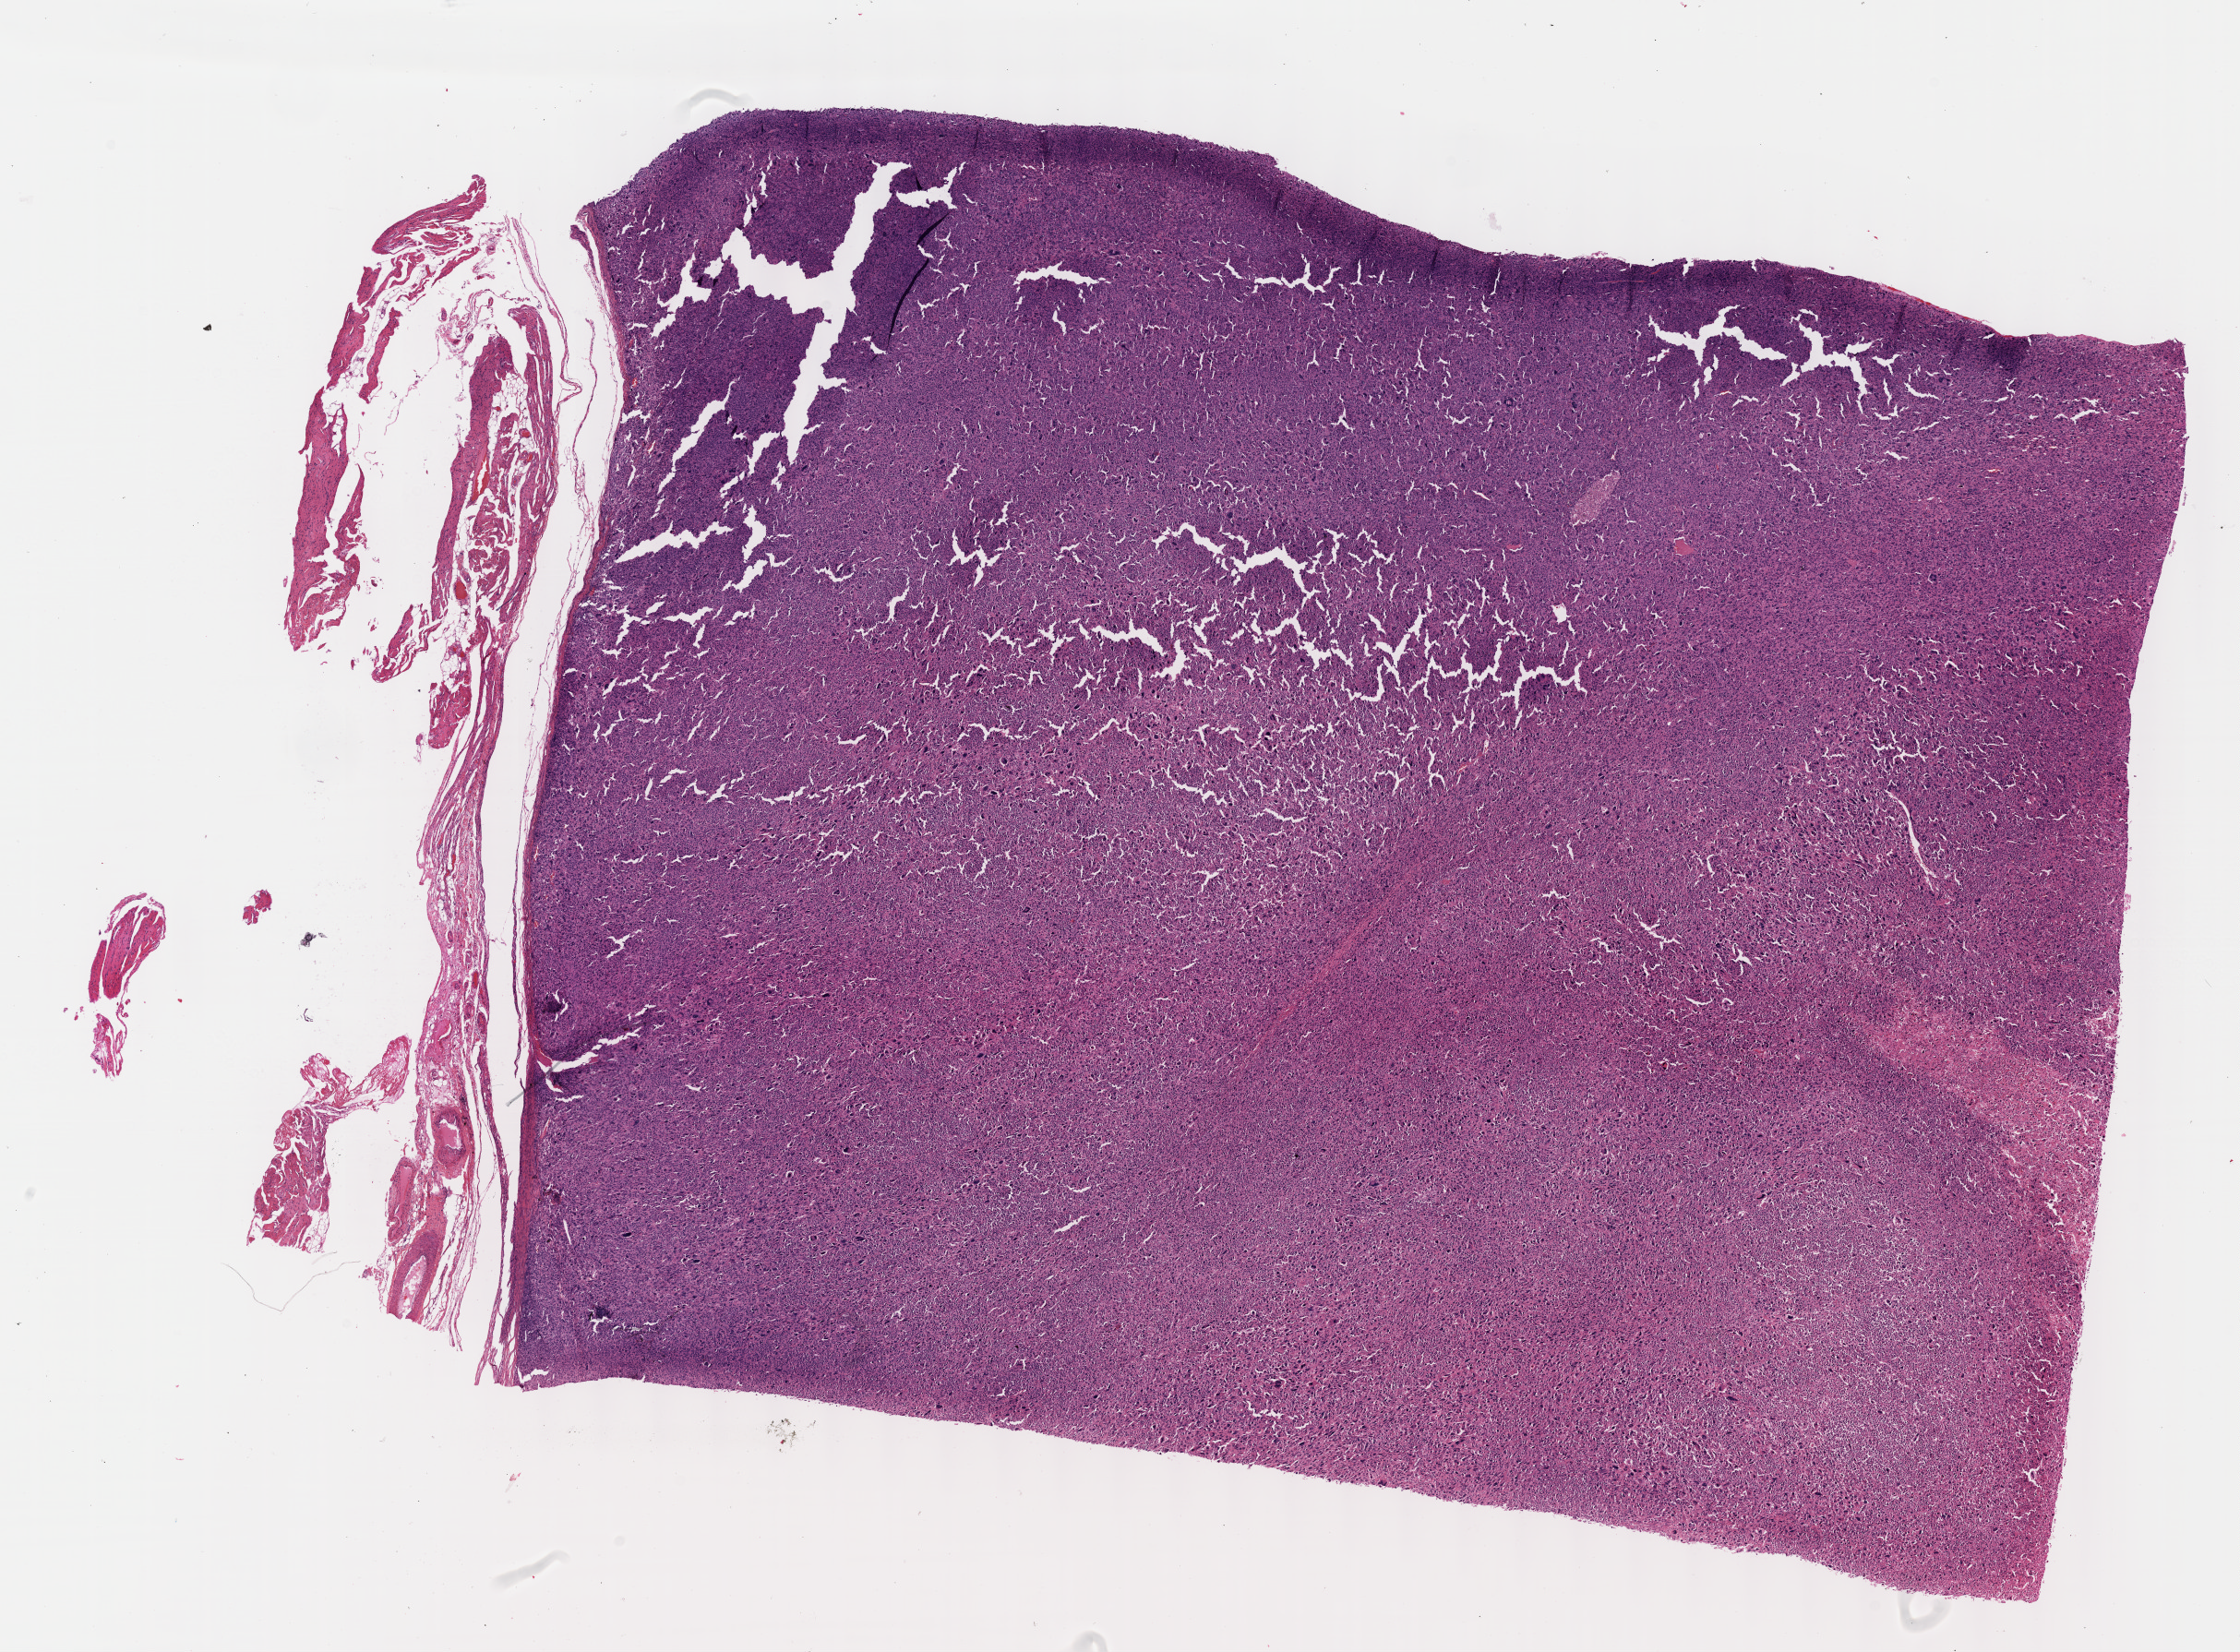
Whole-slide histology image, Hematoxylin and eosin (H&E) stained, whole scanned area (about 19.6 x 14.5 mm) shown as a low-resolution overview, formalin-fixed paraffin-embedded (FFPE) diagnostic section, retroperitoneum and peritoneum, primary tumour sample. Female patient; age at initial diagnosis 64 years.
Pathologic diagnosis: Undifferentiated sarcoma (retroperitoneum).